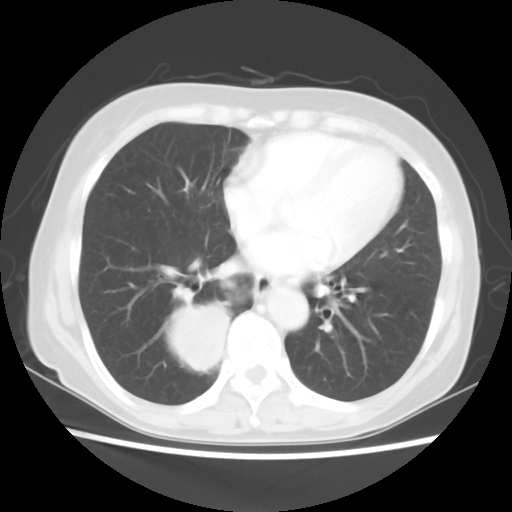
Chest CT, one axial slice; slice 22 of 56 in the series (ordered by position); lung window (W 1500 / L -600 HU); 5 mm slice thickness; 512 × 512 image matrix, field of view 332 × 332 mm. Patient: female, 66 years. From the clinical record (not read from this slice): clinical TNM (as recorded): T2 N3 M0; histopathological grade: G3.
Annotated regions visible in this slice (bounding box drawn by a radiologist):
- lung tumour (recorded histology: small cell carcinoma): bounding box (x1, y1, x2, y2) in pixels: (158, 293, 232, 378)